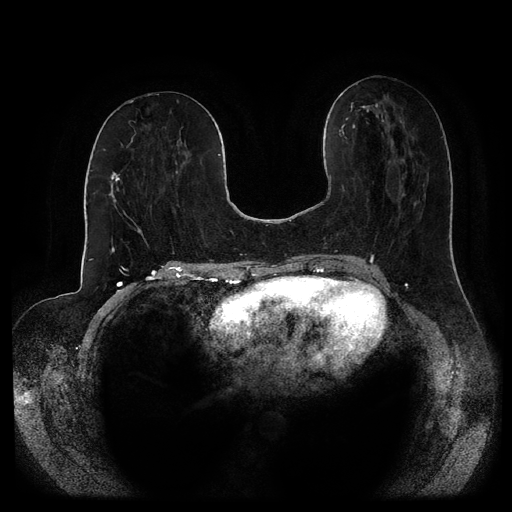
Breast MRI (dynamic contrast-enhanced, multi-phase), one axial slice; position 44 of 116 along the scan axis; dynamic contrast-enhanced series, time point 2 of 5 at this slice position (early post-contrast); 1.5 T; TE 2.6 ms, TR 5.2 ms; 2 mm slice thickness; 512 × 512 image matrix, field of view 380 × 380 mm. Patient: female, 53 years.
Structures marked on this image (semi-automatically segmented with operator editing):
- breast lesion (labelled 'tumour' in the annotation; benign lesions carry a separate 'benign' label): bounding box (x1, y1, x2, y2) in pixels: (110, 172, 121, 183)